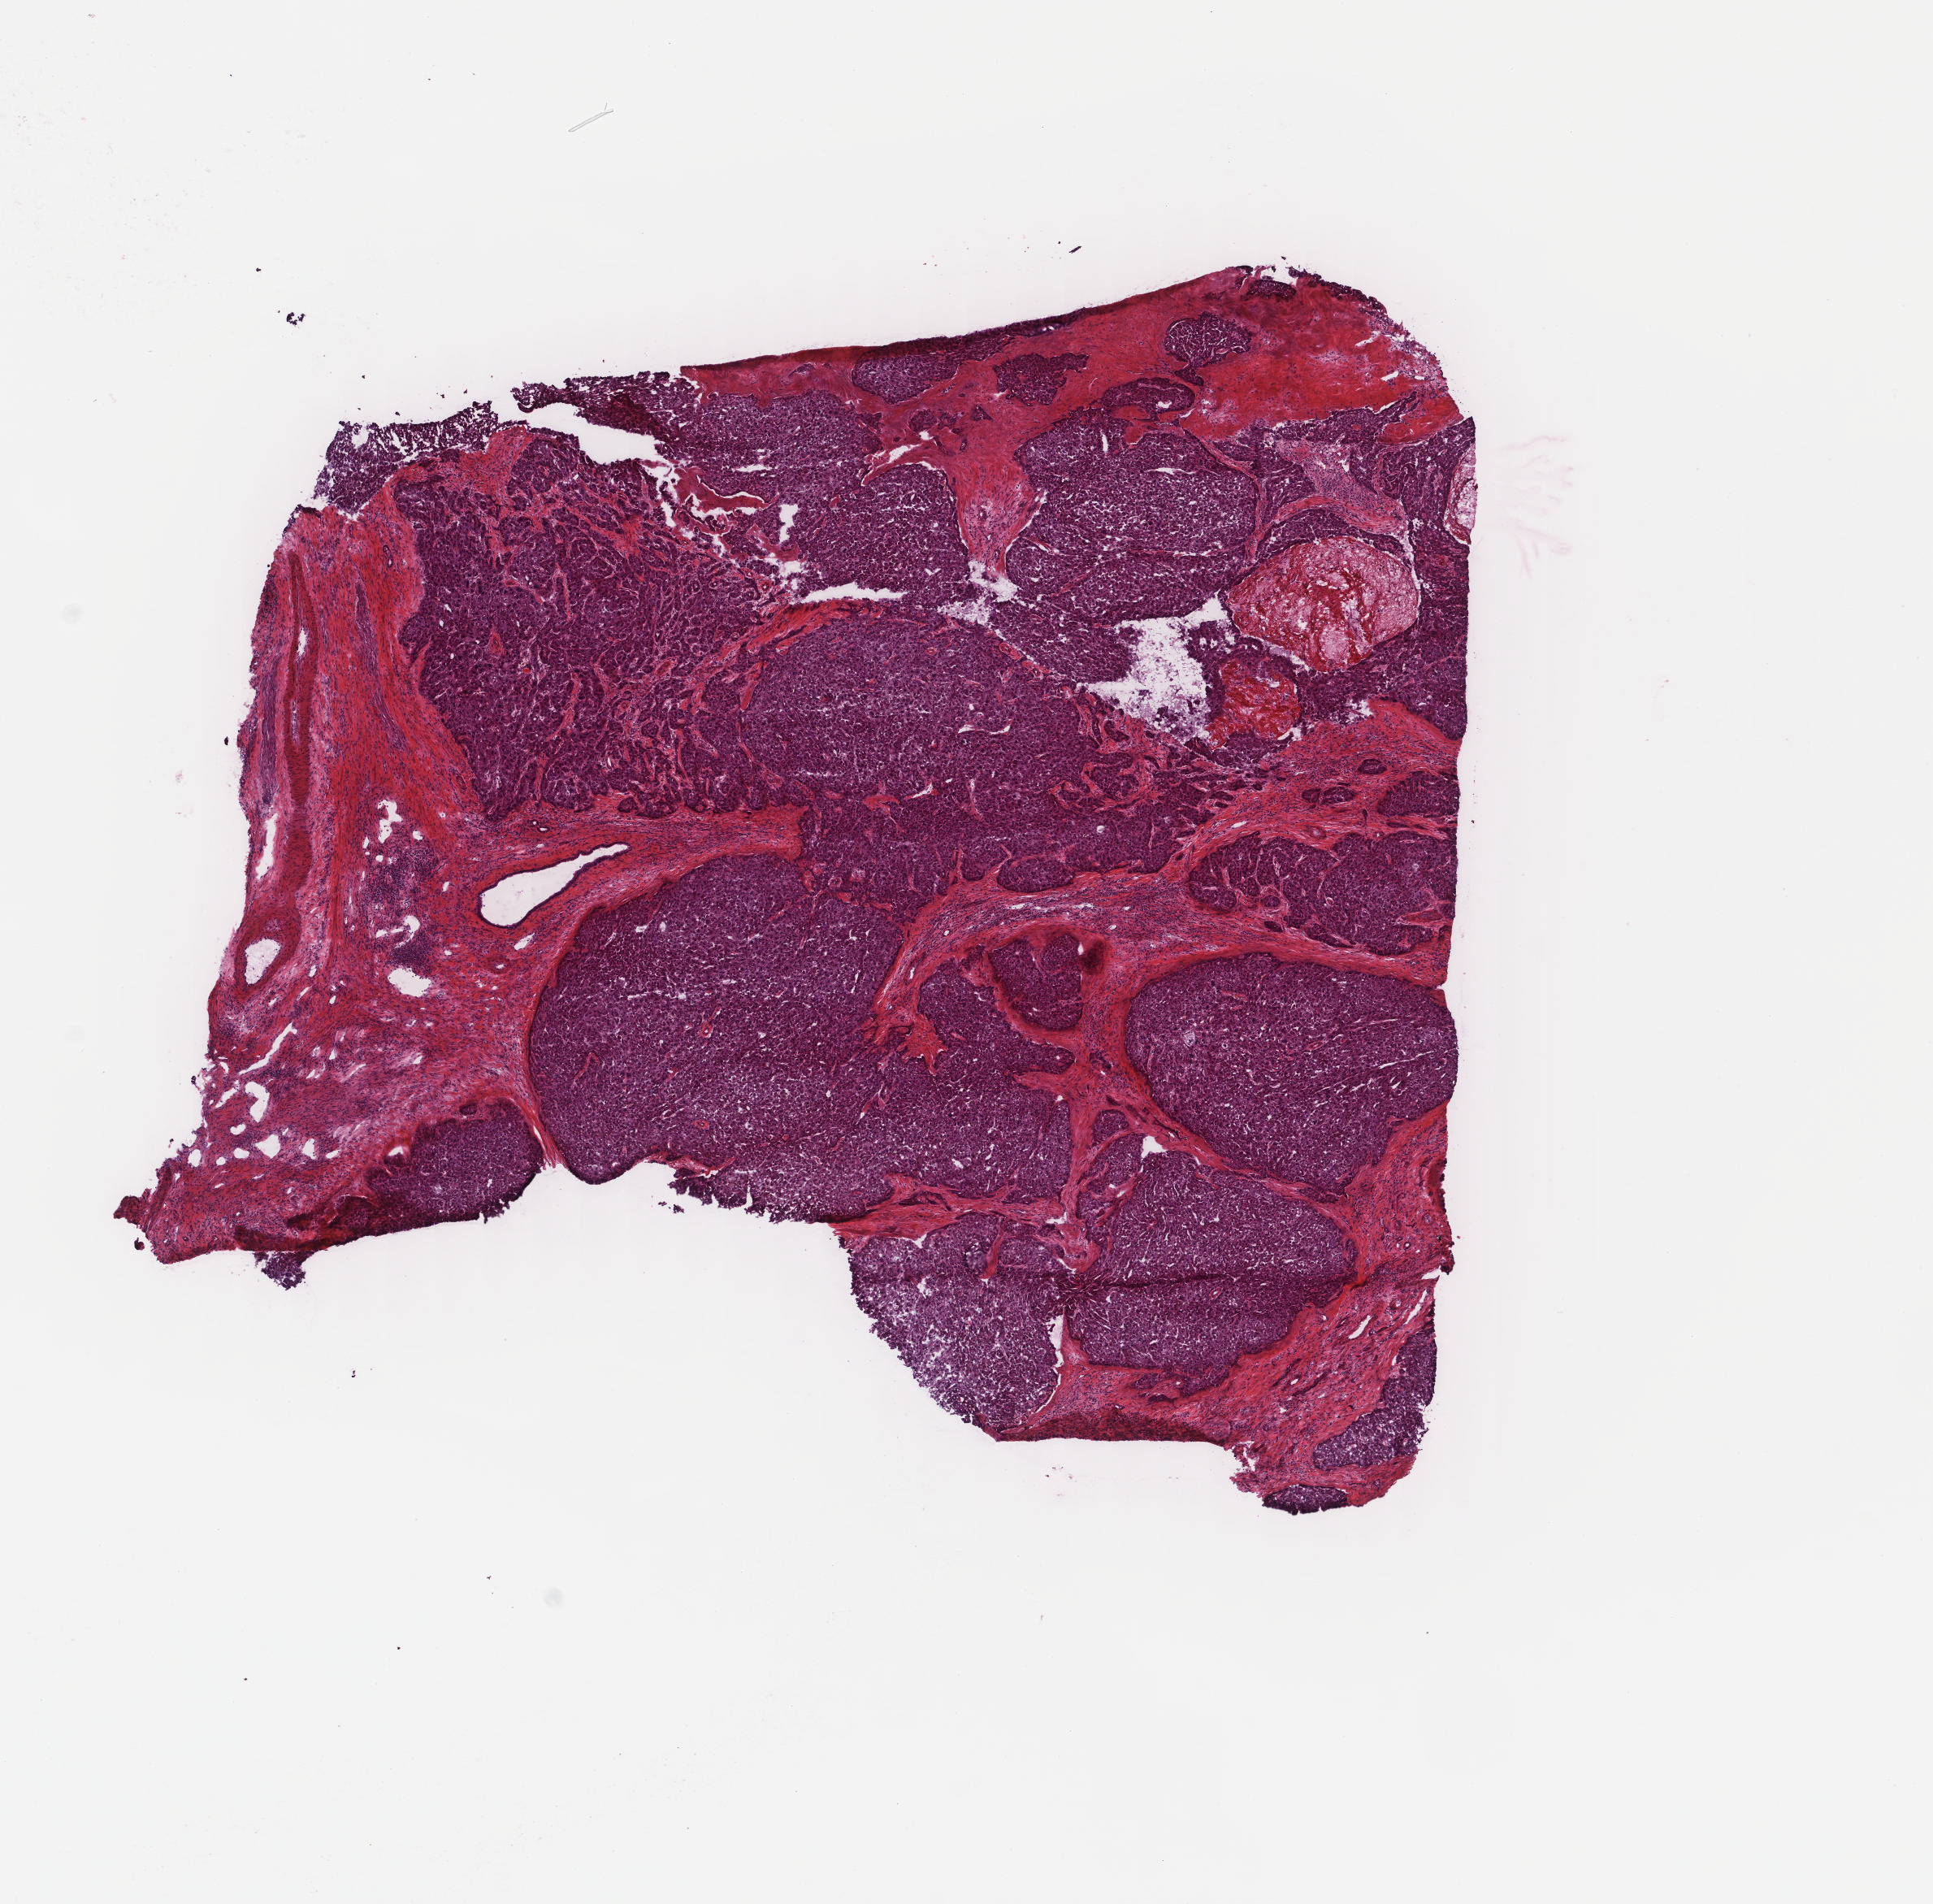
H&E whole-slide image, a low-resolution overview of the entire scanned area, about 9.4 x 9.3 mm, frozen section from the top of the tissue portion, sample: primary tumour, liver. Male patient; age at initial diagnosis 70 years. Pathologist review of this section (percent, as recorded): tumour cells 70%, tumour nuclei 65%.
Pathologic diagnosis: Hepatocellular carcinoma, NOS.